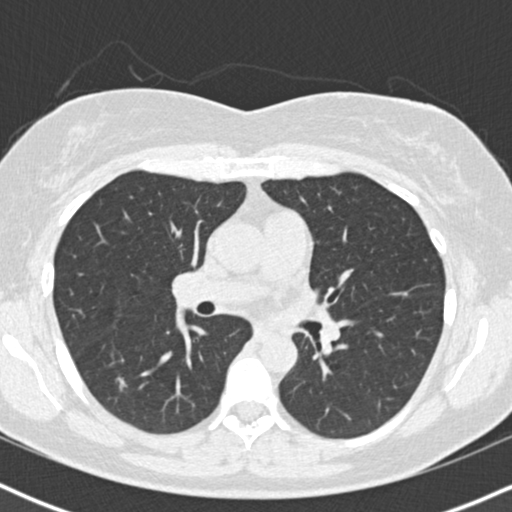
Low-dose screening chest CT, one axial slice; position 97 of 167 along the scan axis; 120 kVp; lung window (W 1500 / L -600 HU); 2 mm slice thickness; 512 × 512 image matrix, field of view 320 × 320 mm.
Outlined on this slice (expert manual segmentation):
- lesion 1 (tumor, lower lobe of right lung): box from (x=117, y=377) to (x=127, y=391) px